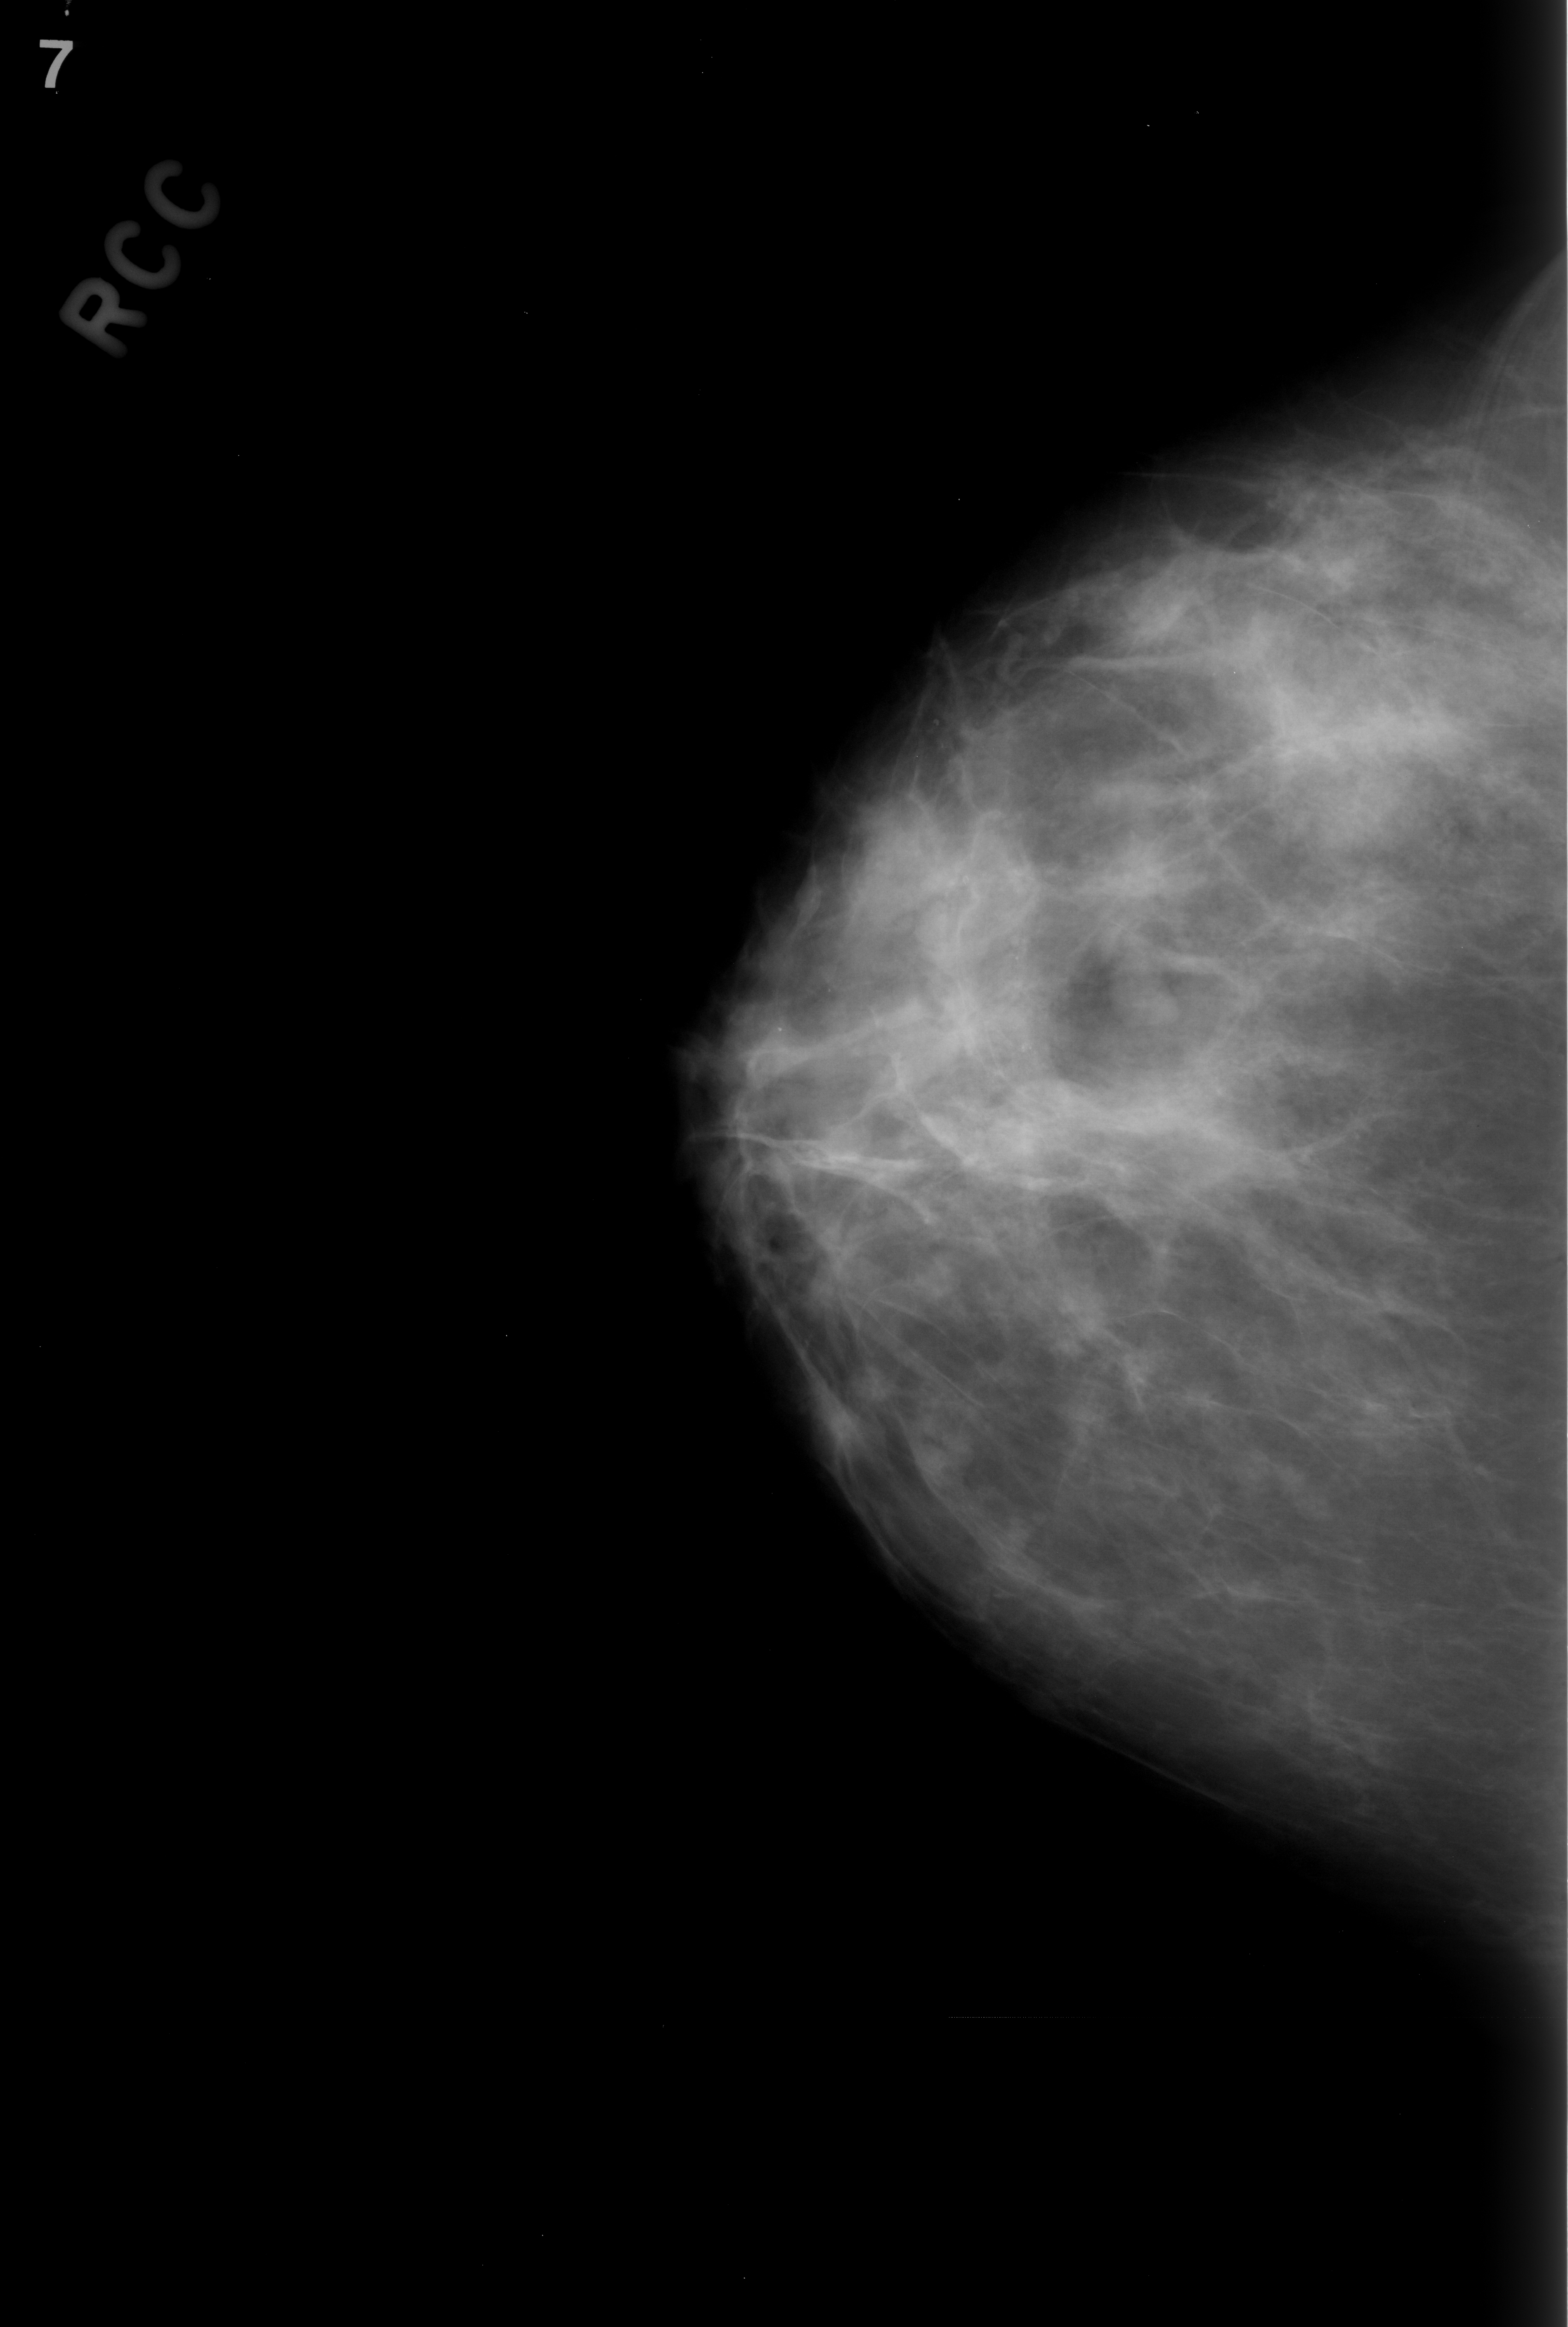
Scanned film-screen mammogram; right breast; CC view; BI-RADS breast density category 2 (scale 1–4).
- Marked abnormality: mass, shape lobulated, margins circumscribed; BI-RADS assessment category 3; pathology result (as recorded, not read from the image): benign.